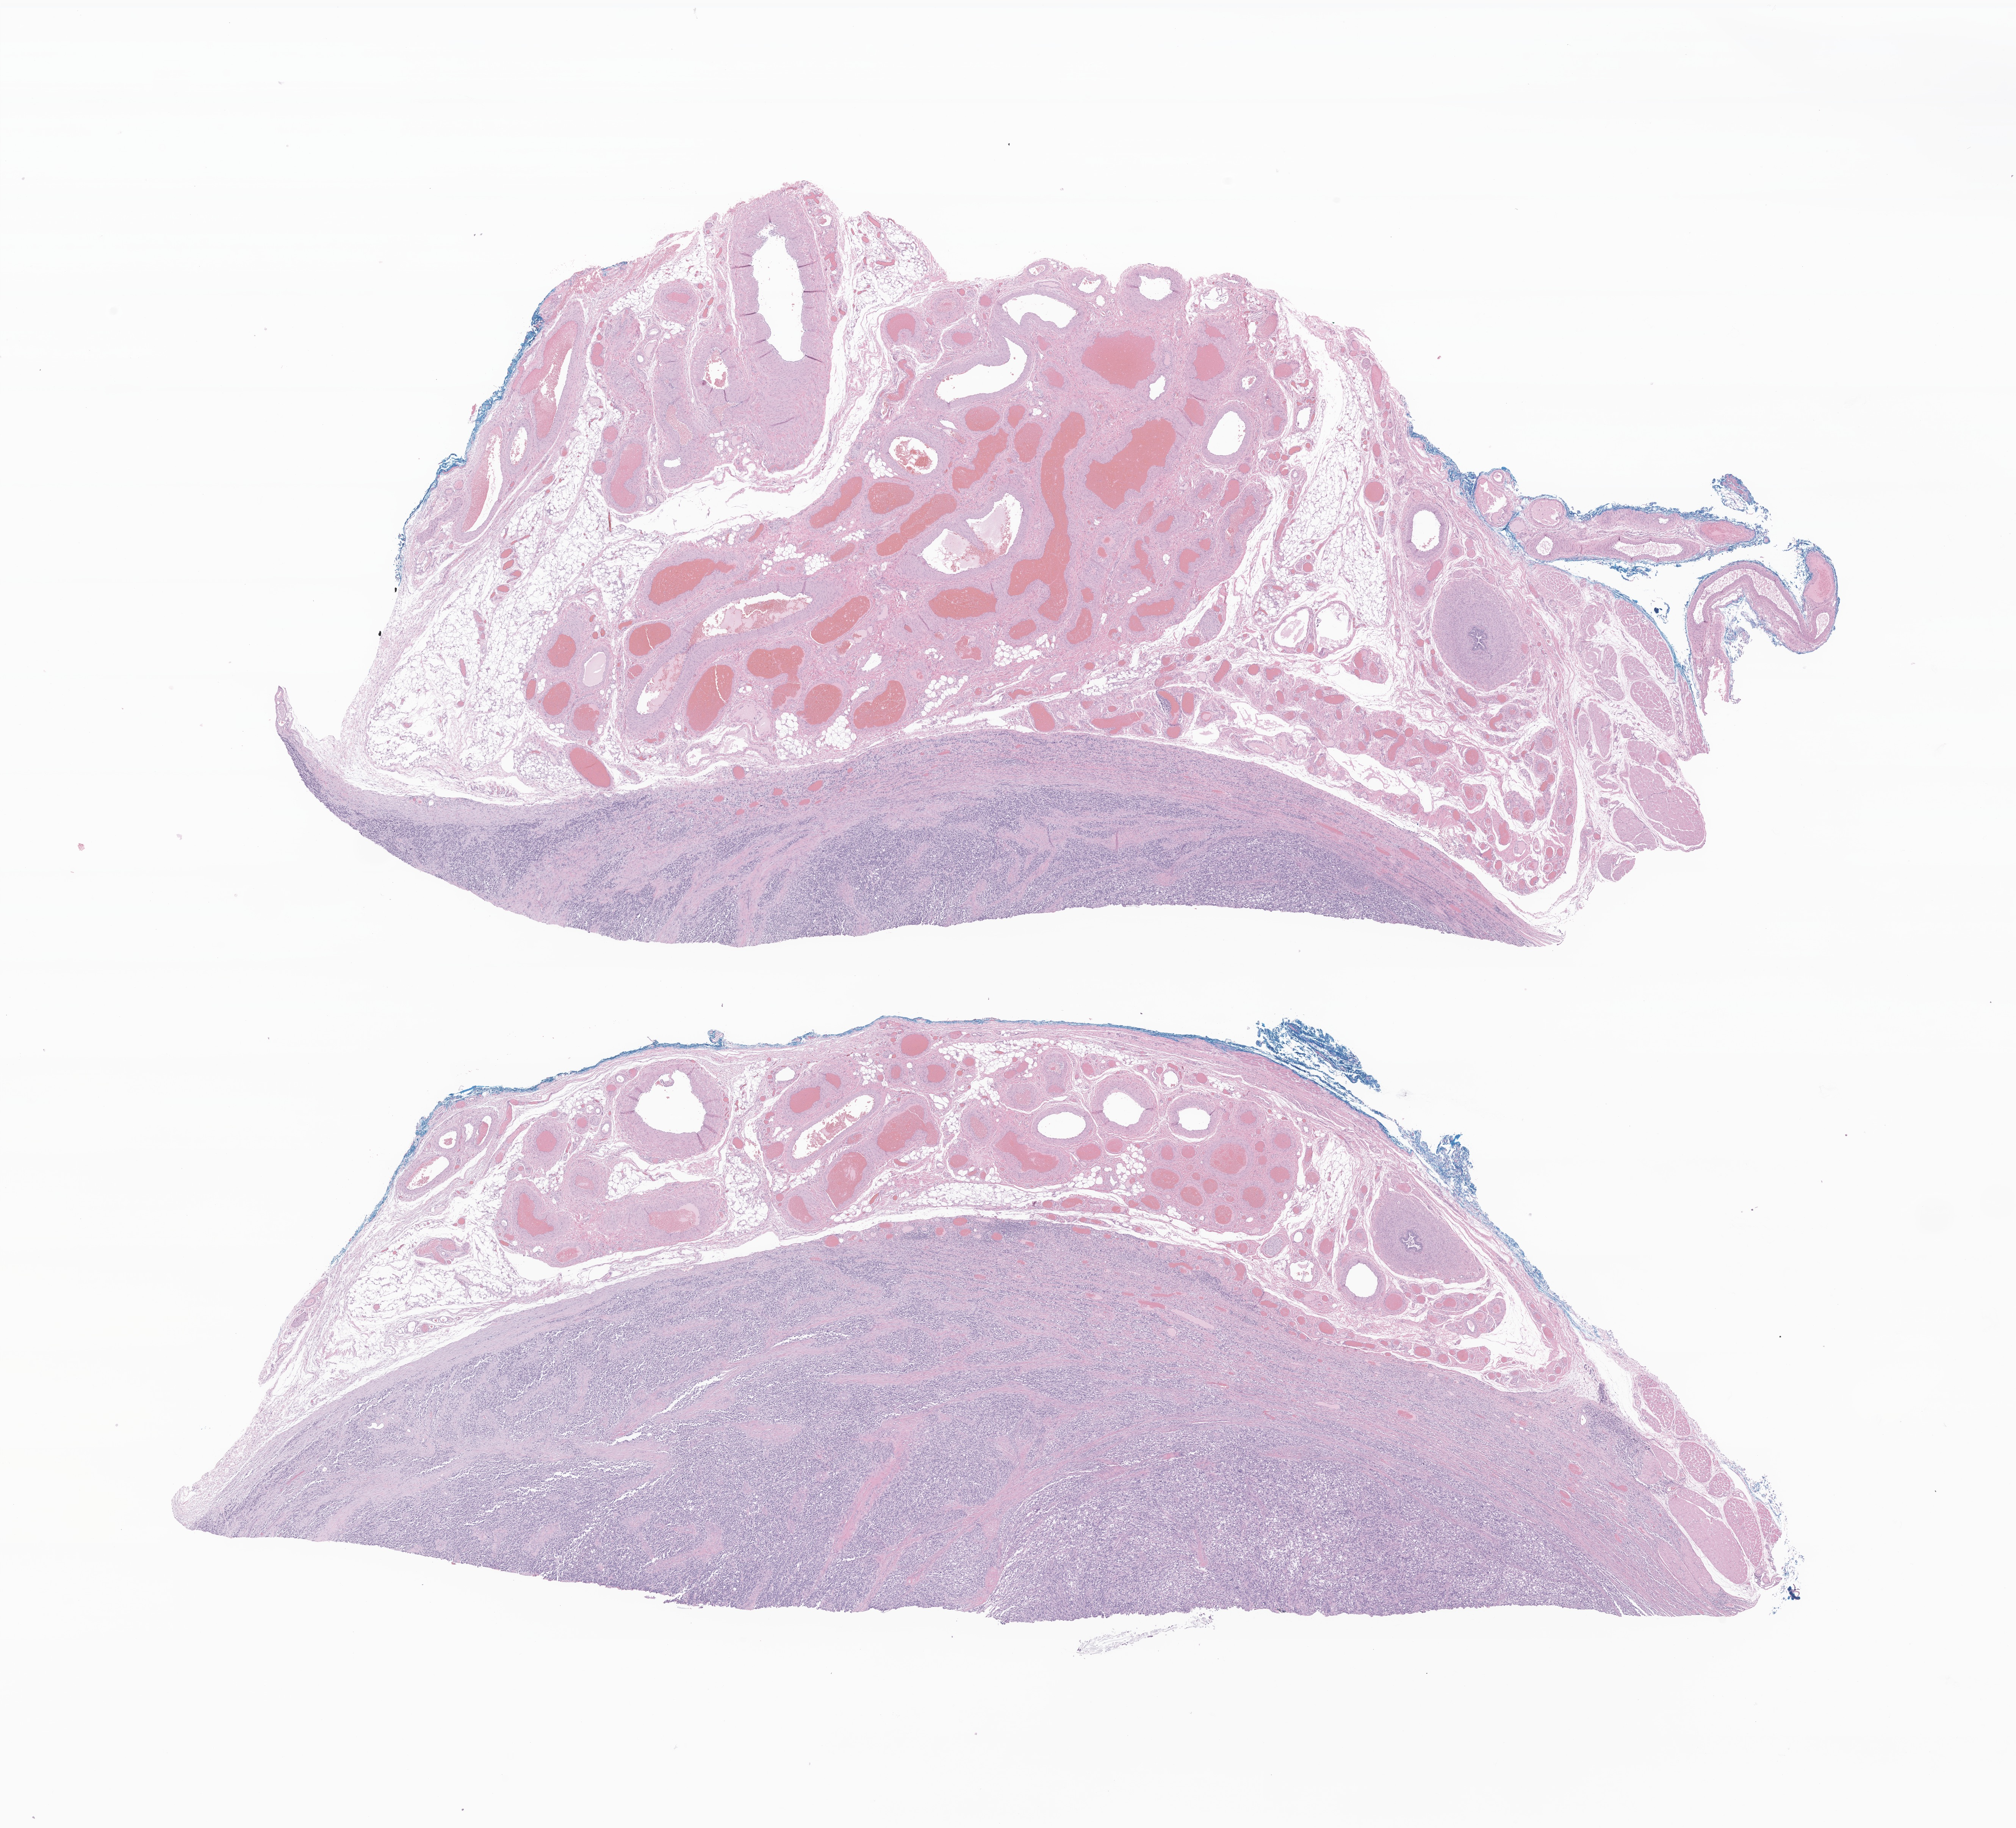
Digitized haematoxylin and eosin-stained section of tumor tissue from the soft tissue of abdomen — whole scanned area (about 22.4 x 20.3 mm) shown as a low-resolution overview, formalin-fixed, paraffin-embedded (FFPE) tissue. Patient male; age 98 months (8 years 2 months).
Diagnosis (ICD-O-3 morphology term): Rhabdomyosarcoma, NOS.